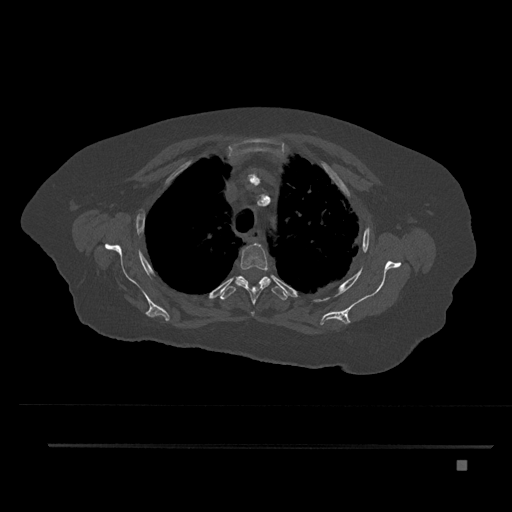
CT including the spine, one axial slice. Position 624 of 797 along the scan axis. Reconstruction kernel Br40s/3. 120 kVp. Bone window (W 1800 / L 400 HU). 0.5 mm slice thickness. 512 × 512 image matrix. Patient: female, 76 years. Case-level facts recorded for this patient, not image findings: primary cancer: lung.
Annotated regions visible in this slice (semi-automatically segmented with operator editing):
- T3 vertebra: bounding box <235,243,271,316> (left, top, right, bottom; pixels)
- T4 vertebra: <219,276,287,300>